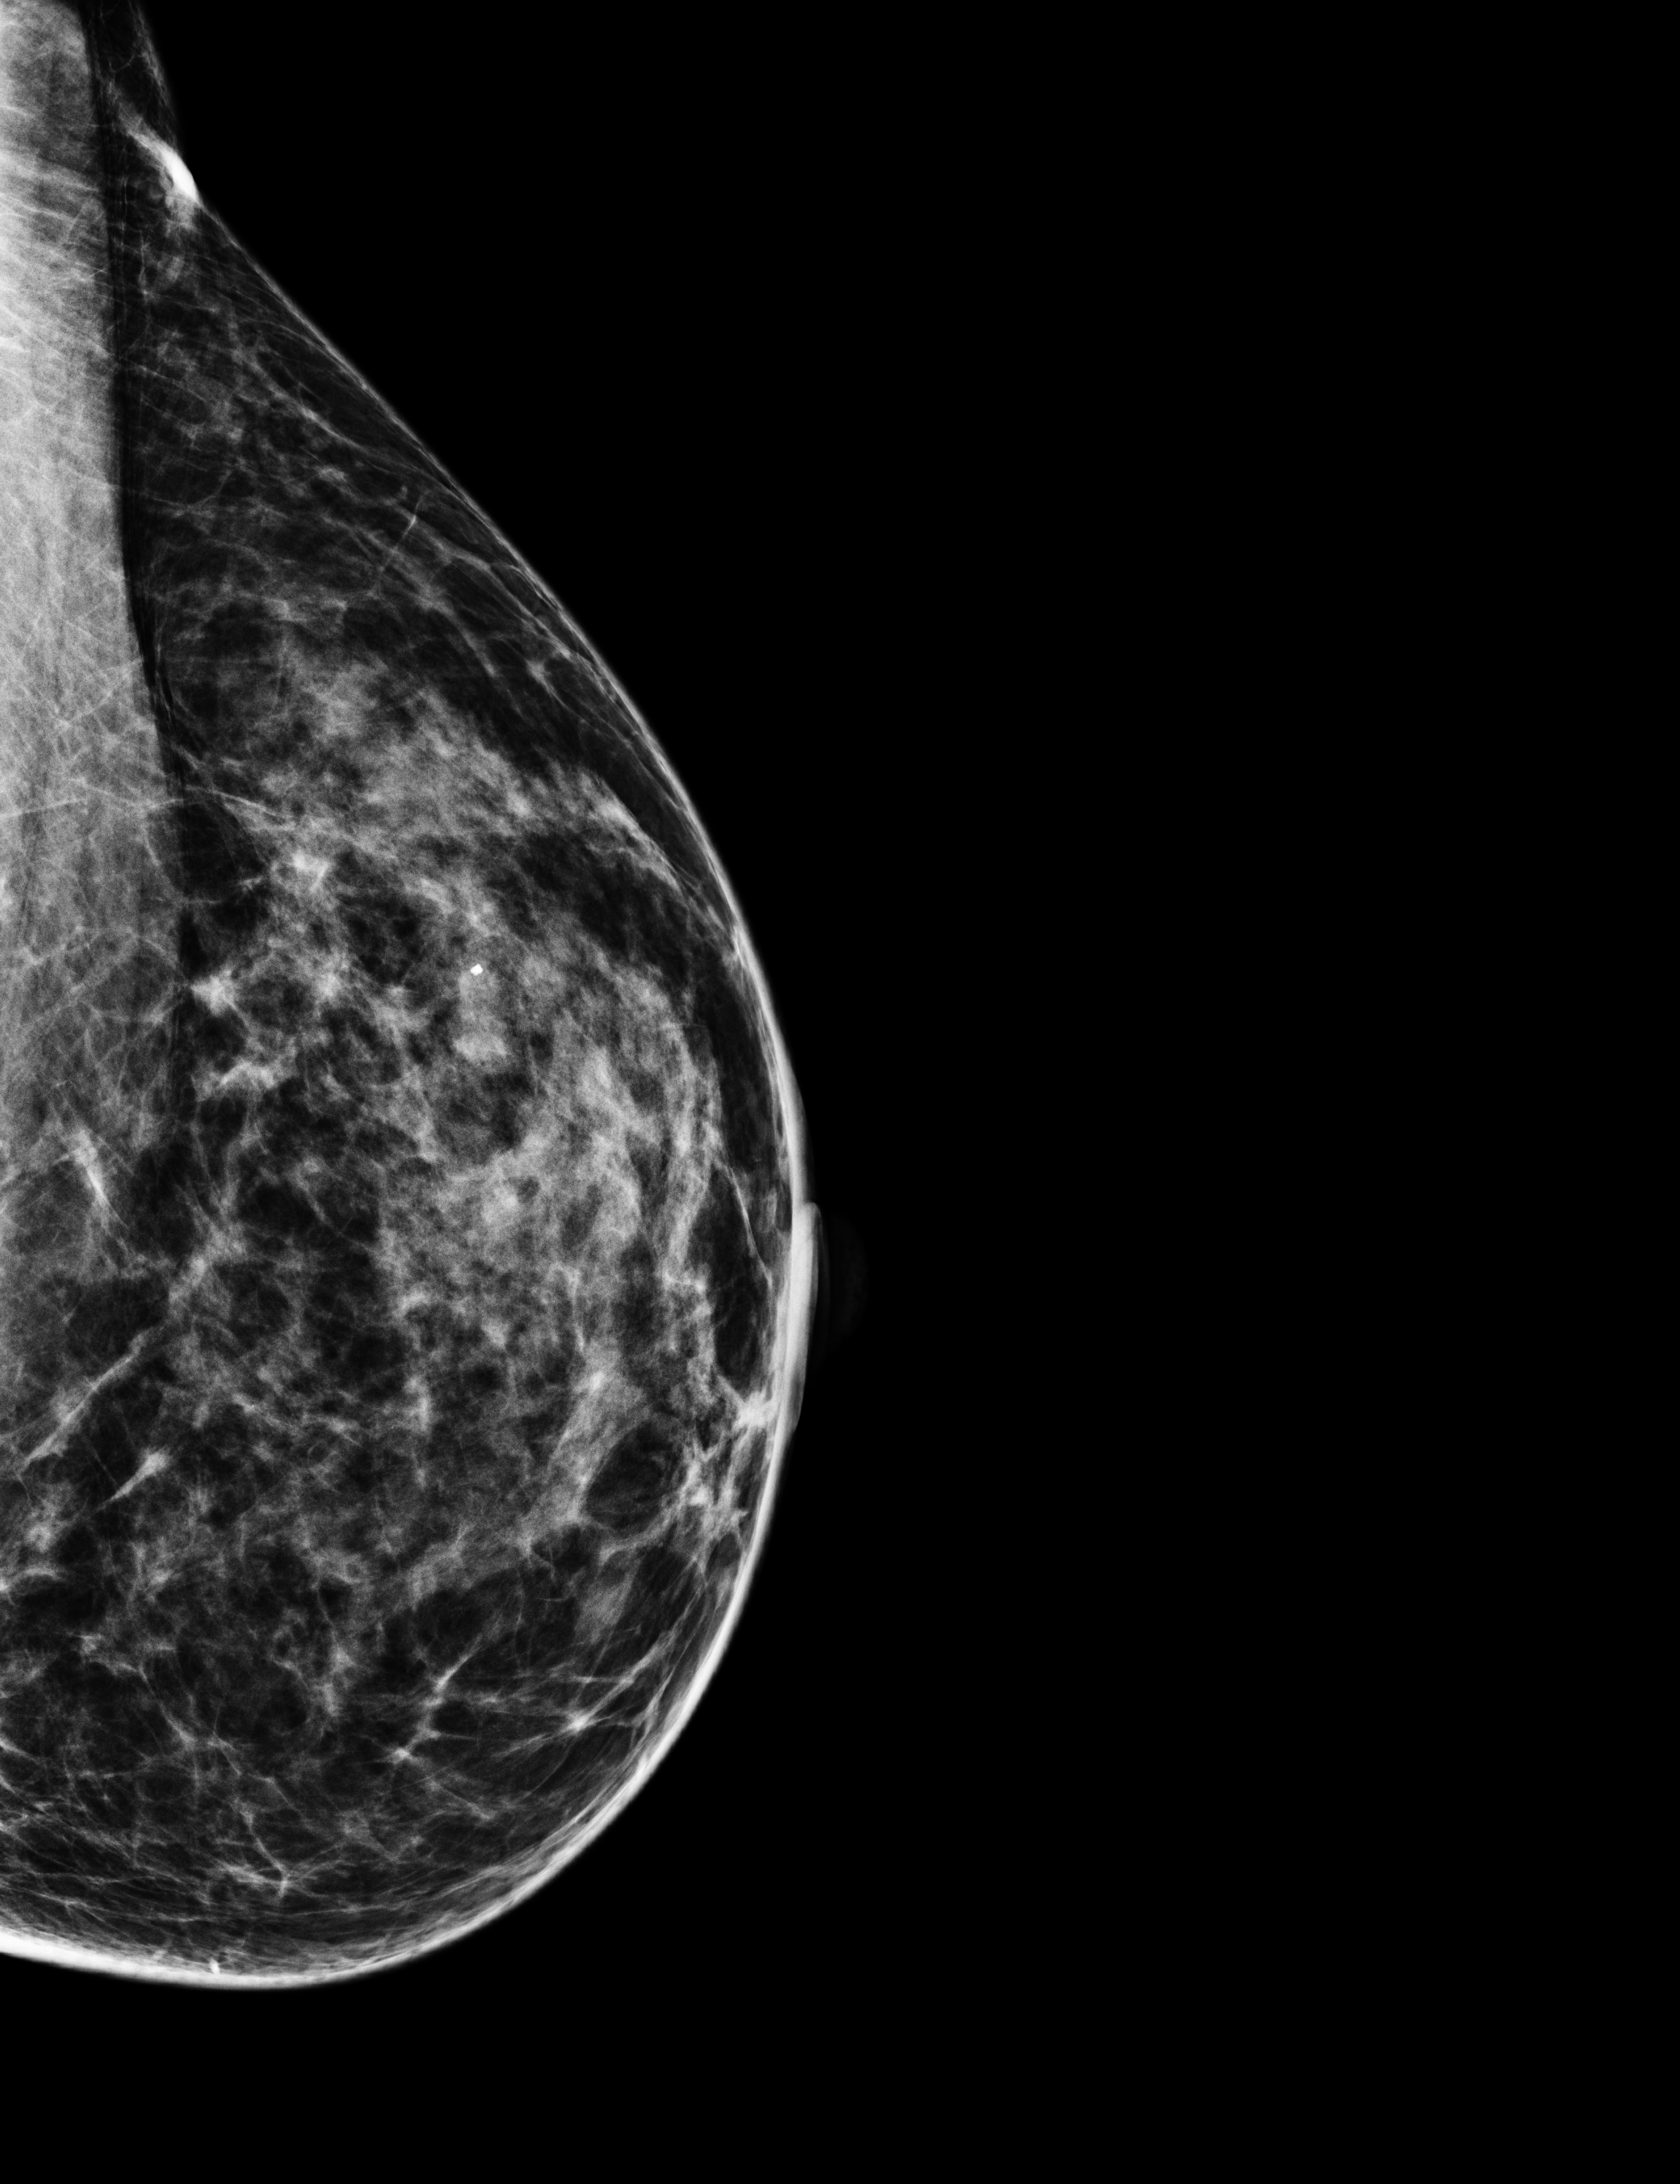
Screening examination. Patient: female, 44 years.
Image type: full-field digital mammogram. Breast: left. Projection: craniocaudal (CC) view.